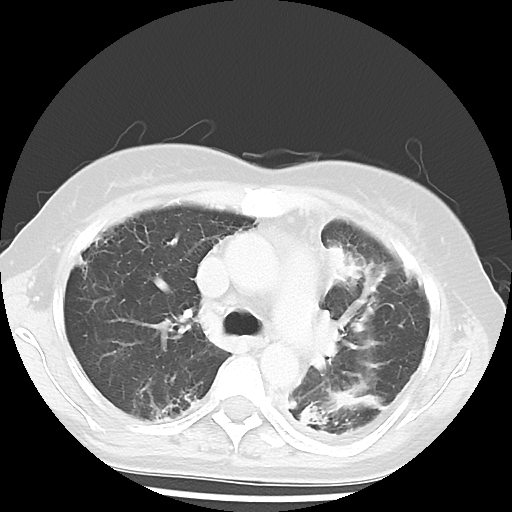
Chest CT, one axial slice; slice 38 of 56 in the series (ordered by position); reconstruction kernel LUNG; 120 kVp; lung window (W 1500 / L -600 HU); 5 mm slice thickness; 512 × 512 image matrix, field of view 309 × 309 mm. Patient: female, 56 years. Case-level facts recorded for this patient, not image findings: clinical TNM (as recorded): T1c N0 M1.
Outlined on this slice (rectangle marked by the reading radiologist):
- lung tumour (recorded histology: adenocarcinoma): bounding box (x1, y1, x2, y2) in pixels: (322, 245, 357, 293)